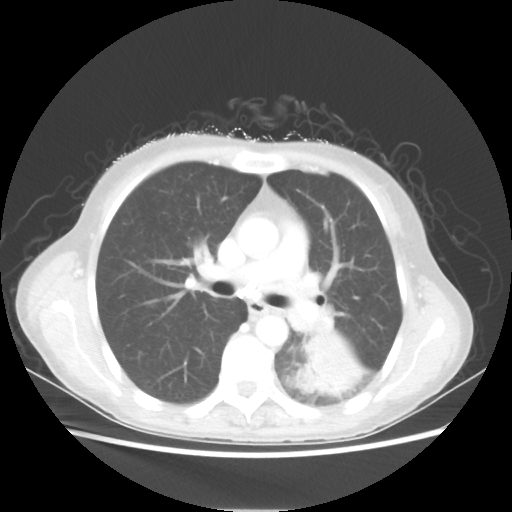
Chest CT, one axial slice; position 33 of 56 along the scan axis; reconstruction kernel STANDARD; lung window (W 1500 / L -600 HU); 5 mm slice thickness; 512 × 512 image matrix, field of view 360 × 360 mm. Female patient, age 53 years. Case-level facts recorded for this patient, not image findings: clinical TNM (as recorded): T3 N0 M0.
Outlined on this slice (rectangle marked by the reading radiologist):
- lung tumour (recorded histology: adenocarcinoma): box from (x=294, y=335) to (x=365, y=397) px